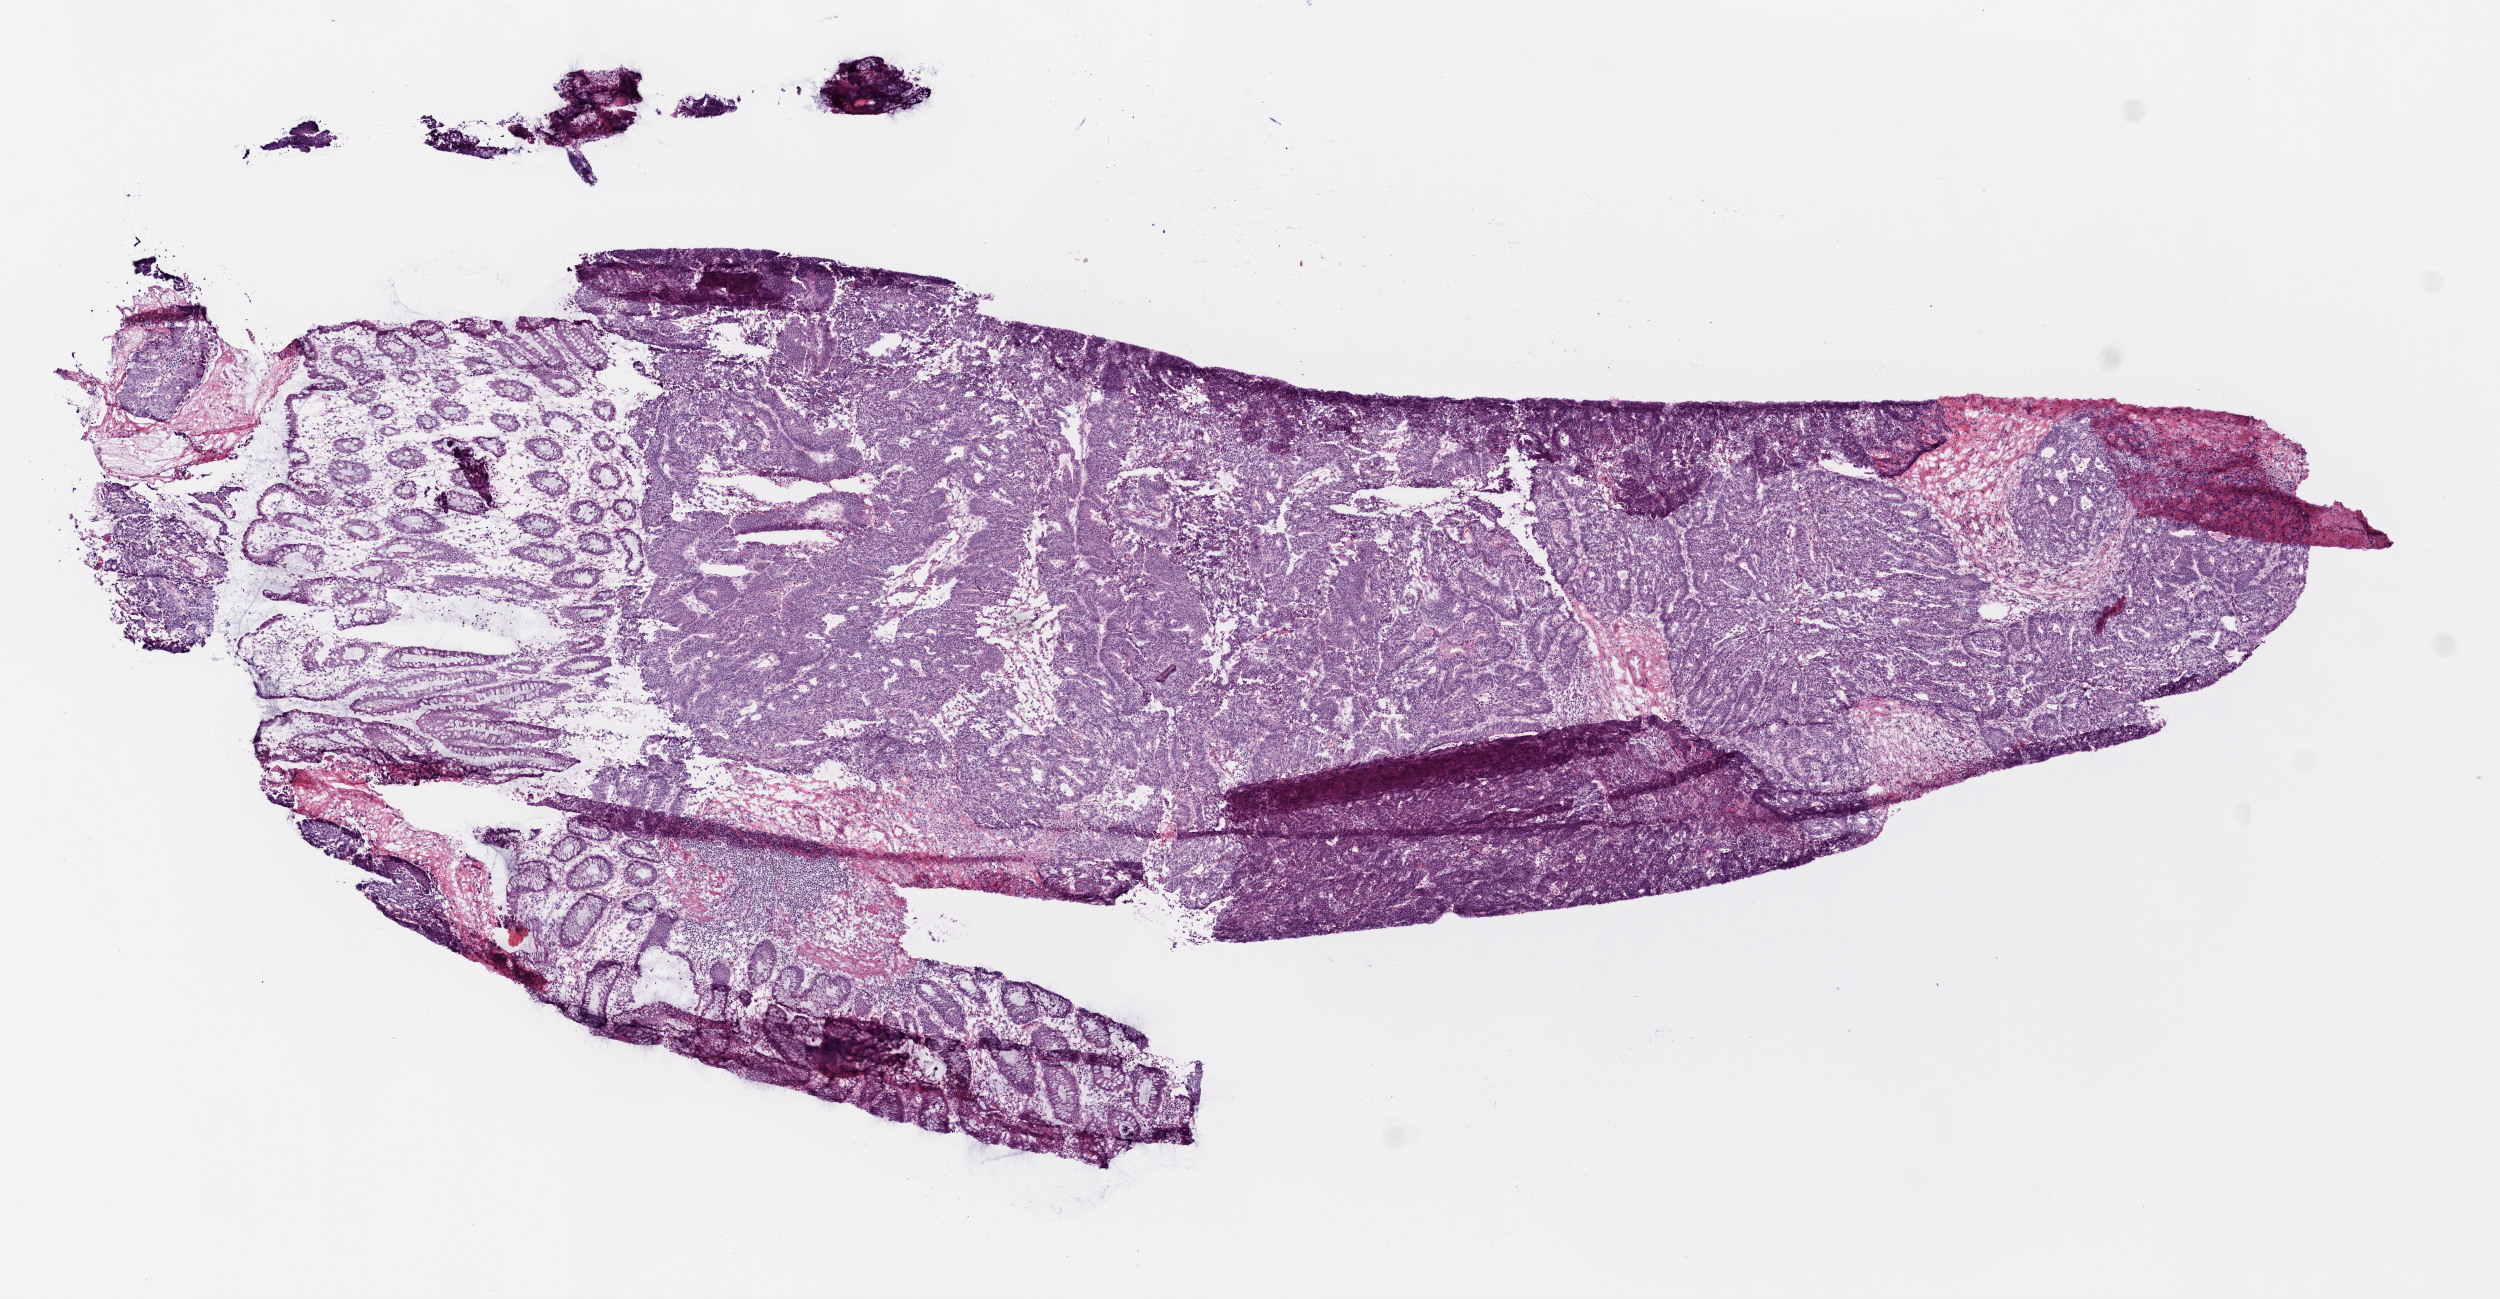
Digitized Hematoxylin and eosin (H&E) stained tissue section (whole slide) — whole scanned area (about 10.0 x 5.2 mm, acquisition: 20x scan) shown as a low-resolution overview, frozen section, rectum, primary tumour sample. Female, age 79 years at initial diagnosis. Slide review estimates, as recorded: tumour cells 68%, tumour nuclei 85%, normal cells 20%, stromal cells 10%, necrosis 2%.
- diagnosis: Adenocarcinoma, NOS
- AJCC pathologic stage: IIA (6th edition)
- lymph nodes positive (case pathology): 0 of 16 examined